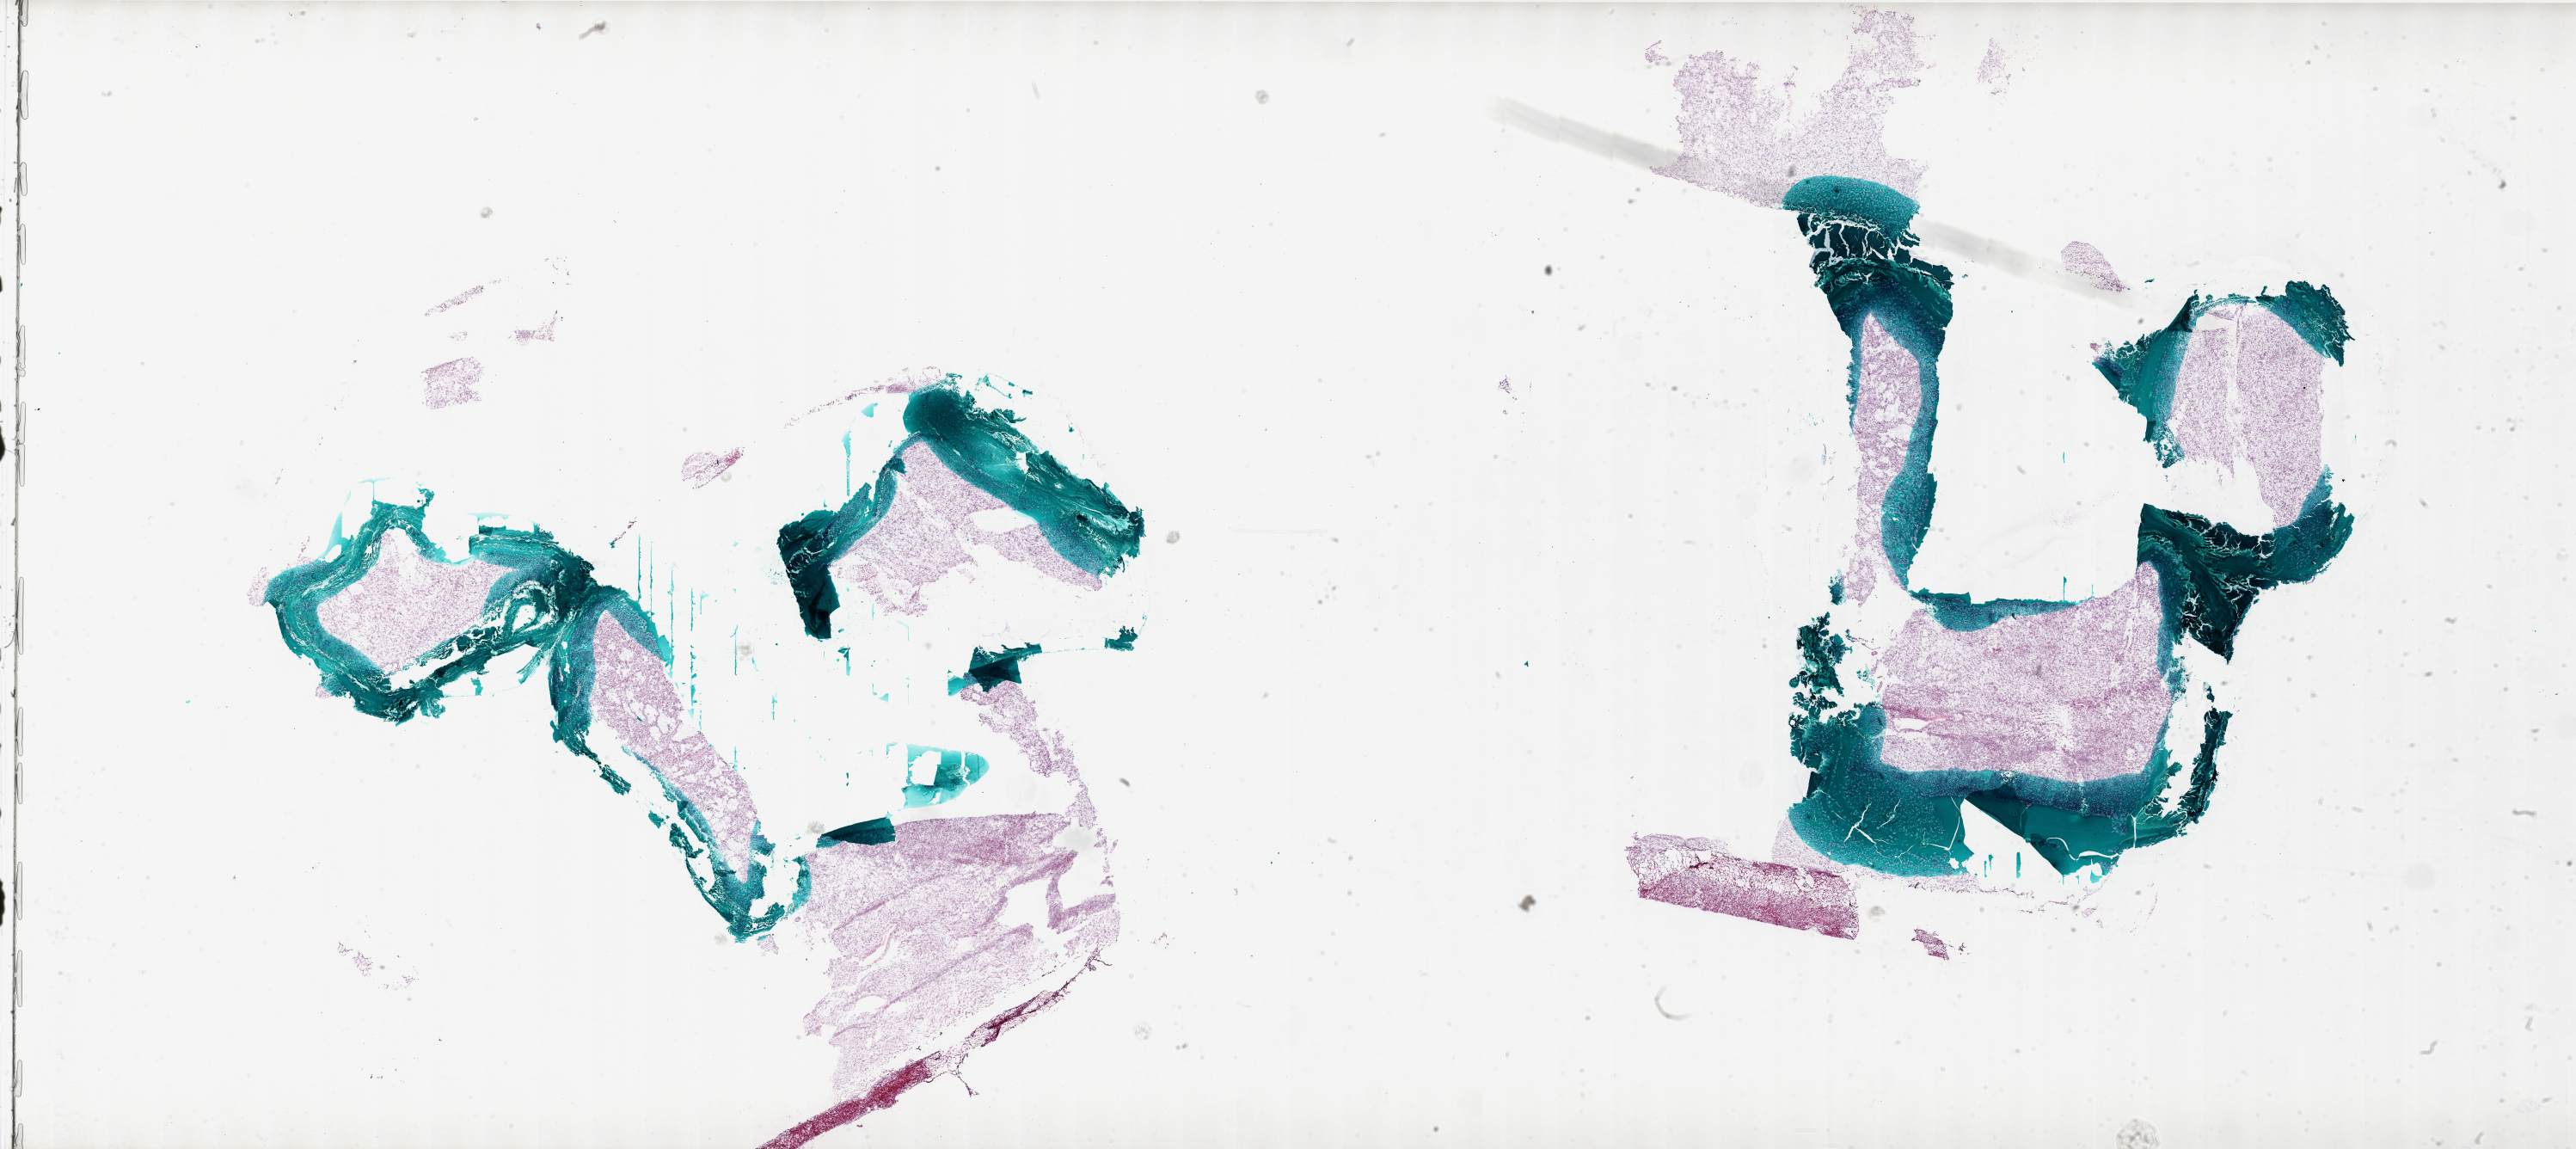
Hematoxylin and eosin (H&E) stained whole-slide image, shown as a low-resolution overview of the whole scanned area (about 48.0 x 21.4 mm). Frozen section from the bottom of the tissue portion. Brain, primary tumour sample. Patient: male, age at initial diagnosis 28 years. Slide review estimates, as recorded: tumour cells 95%, tumour nuclei 100%, normal cells 0%, stromal cells 0%, necrosis 7%.
Diagnosis: Glioblastoma.